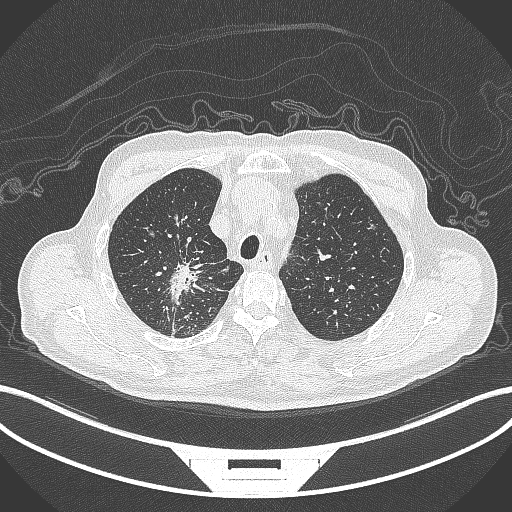
Chest CT, one axial slice; slice 303 of 407 in the series (ordered by position); lung window (W 1500 / L -600 HU); 1 mm slice thickness; 512 × 512 image matrix. Patient: male, 69 years. Case-level facts recorded for this patient, not image findings: clinical TNM (as recorded): T1c N1 M1.
Annotated regions visible in this slice (bounding box drawn by a radiologist):
- lung tumour (recorded histology: adenocarcinoma): bounding box <162,253,202,309> (left, top, right, bottom; pixels)